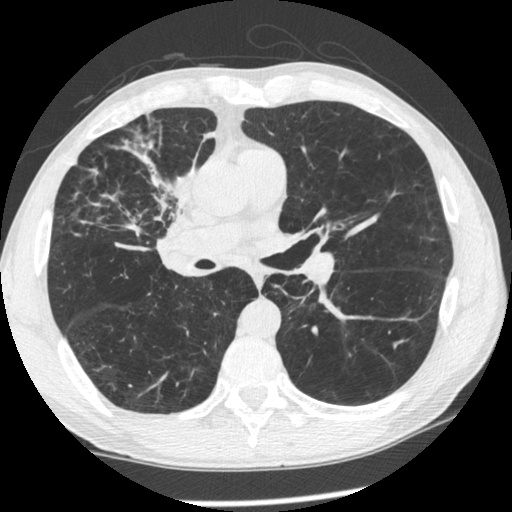
Low-dose screening chest CT, one axial slice; reconstruction kernel STANDARD; lung window (W 1500 / L -600 HU); 1.25 mm slice thickness; 512 × 512 image matrix, field of view 340 × 340 mm.
Annotated regions visible in this slice (expert manual segmentation):
- lesion 1 (tumor, upper lobe of right lung): box from (x=131, y=150) to (x=197, y=234) px